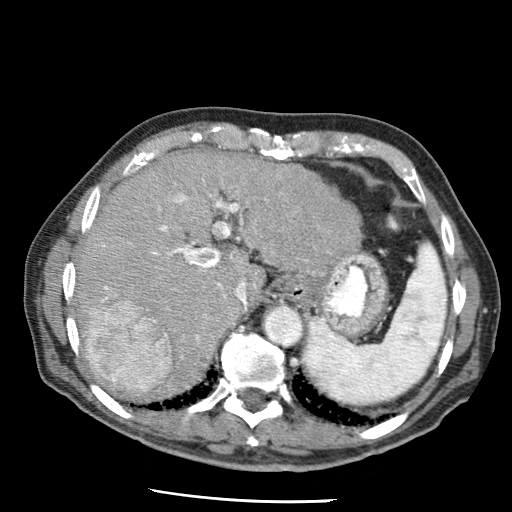
Contrast-enhanced abdominal CT (liver protocol), one axial slice; slice 48 of 79 in the series (ordered by position); reconstruction kernel STANDARD; 120 kVp; soft-tissue window (W 400 / L 40 HU); 512 × 512 image matrix, field of view 320 × 320 mm. From the clinical record (not read from this slice): diagnosis: hepatocellular carcinoma (patient treated with transarterial chemoembolisation; whether this scan precedes or follows treatment is not stated here); TNM stage (as recorded): Stage-IIIA; Child-Pugh class: A; tumour differentiation: moderately differentiated; tumour nodularity: multinodular.
Structures marked on this image (semi-automatically segmented with operator editing):
- liver parenchyma outside the tumour (the mass and vessels are separate outlines, so this box may not span the whole liver): bounding box [x1, y1, x2, y2] px = [74, 152, 362, 394]
- mass: [85, 300, 171, 394]
- liver vessels: [101, 180, 242, 303]